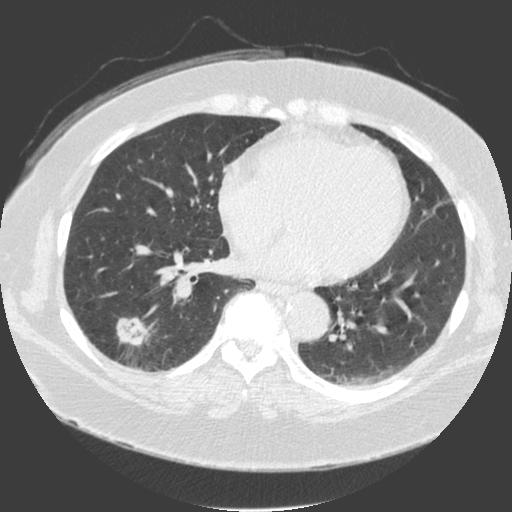
Low-dose screening chest CT, axial slice; third annual screen; lung window (W 1500 / L -600 HU); 2 mm slice thickness; 512 × 512 image matrix, field of view 370 × 370 mm. Female, age 56 years at enrolment. Current smoker at enrolment.
Expert-annotated lung lesion, box from (x=102, y=303) to (x=157, y=355) px. The screening reader recorded 4 non-calcified nodules or masses ≥4 mm on this exam; which of them this box marks is not recorded.